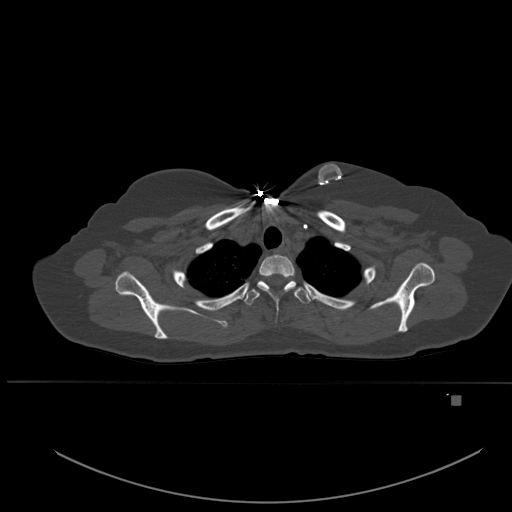
CT including the spine, one axial slice; position 412 of 651 along the scan axis; bone window (W 1800 / L 400 HU); 1.5 mm slice thickness; 512 × 512 image matrix. Female patient, age 49 years. Case-level facts recorded for this patient, not image findings: primary cancer: breast.
Outlined on this slice (semi-automatically segmented with operator editing):
- T1 vertebra: bounding box <258,255,296,310> (left, top, right, bottom; pixels)
- T2 vertebra: <244,280,312,305>